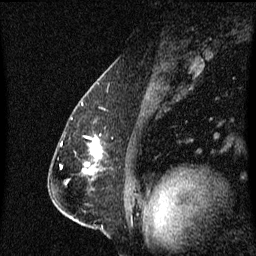
Breast MRI (dynamic contrast-enhanced), one sagittal slice; slice 43 of 60 in the series (ordered by position); dynamic contrast-enhanced series, image 2 of 3 at this slice position (ordered by acquisition); 1.5 T; TE 4.2 ms, TR 8.4 ms; 256 × 256 image matrix, field of view 200 × 200 mm. Female patient, age 57 years. Case-level facts recorded for this patient, not image findings: setting: breast cancer imaged before/during neoadjuvant chemotherapy; receptor status: HR-positive, HER2-negative.
Structures marked on this image (semi-automatic segmentation, software-assisted and operator-edited):
- analysis volume of interest (the breast-tissue region the enhancement analysis was run in; not a lesion): bounding box (x1, y1, x2, y2) in pixels: (82, 140, 101, 175)
- tumour enhancement mask (voxels above the 70 % enhancement threshold inside the analysis volume of interest): (89, 140, 101, 171)